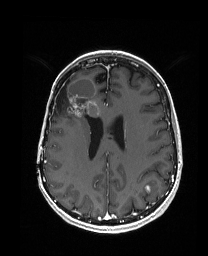
Brain MRI from a brain-tumour surgery series, one axial slice. T1-weighted post-contrast. 1 mm slice thickness. 208 × 256 image matrix, field of view 203 × 250 mm. Case-level facts recorded for this patient, not image findings: histopathology: Metastatic Carcinoma from Breast primary; tumour location: Right Frontal.
Annotated regions visible in this slice (outlined manually by an expert reader):
- previous resection cavity: bounding box [x1, y1, x2, y2] px = [53, 80, 70, 114]
- tumour: [55, 77, 104, 128]